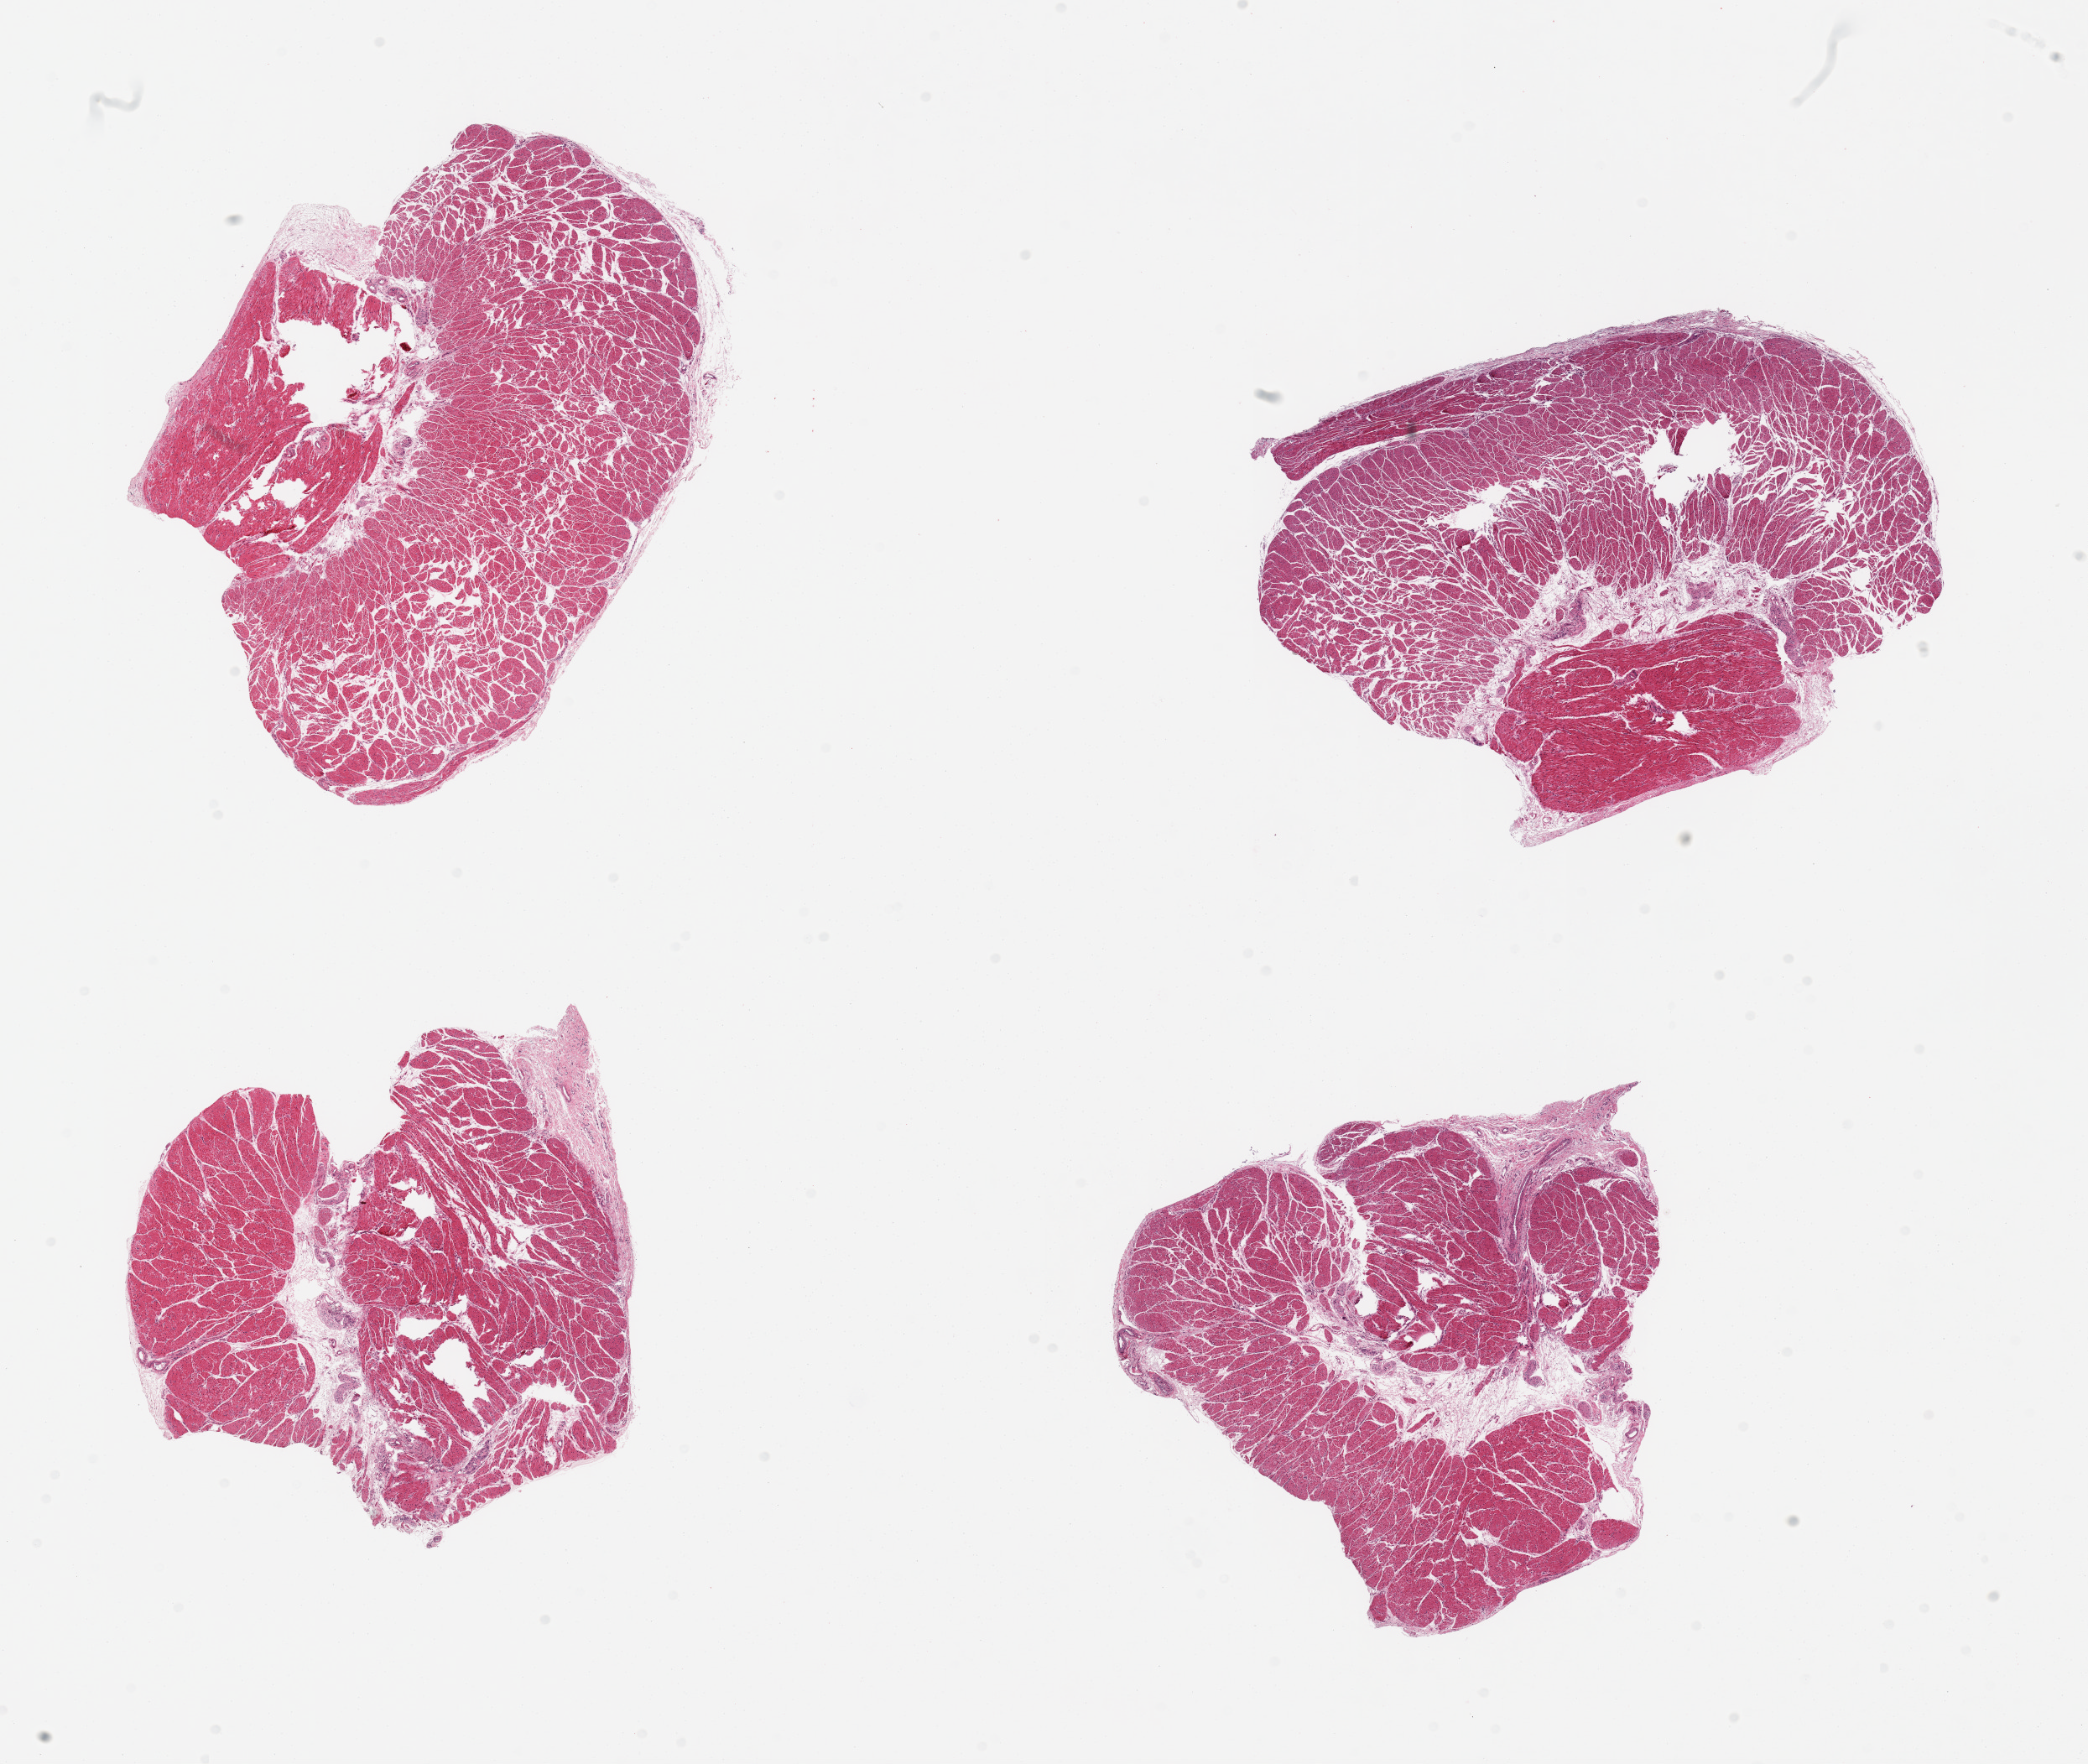
Whole-slide image, hematoxylin and eosin (H&E) stain — shown as a low-resolution overview of the whole scanned area (about 19.7 x 16.6 mm), PAXgene-fixed, paraffin-embedded tissue, sampled site (target tissue): esophageal muscle, tissue donor sample. Female donor.
Reviewer comment on this tissue sample: 4 pieces.